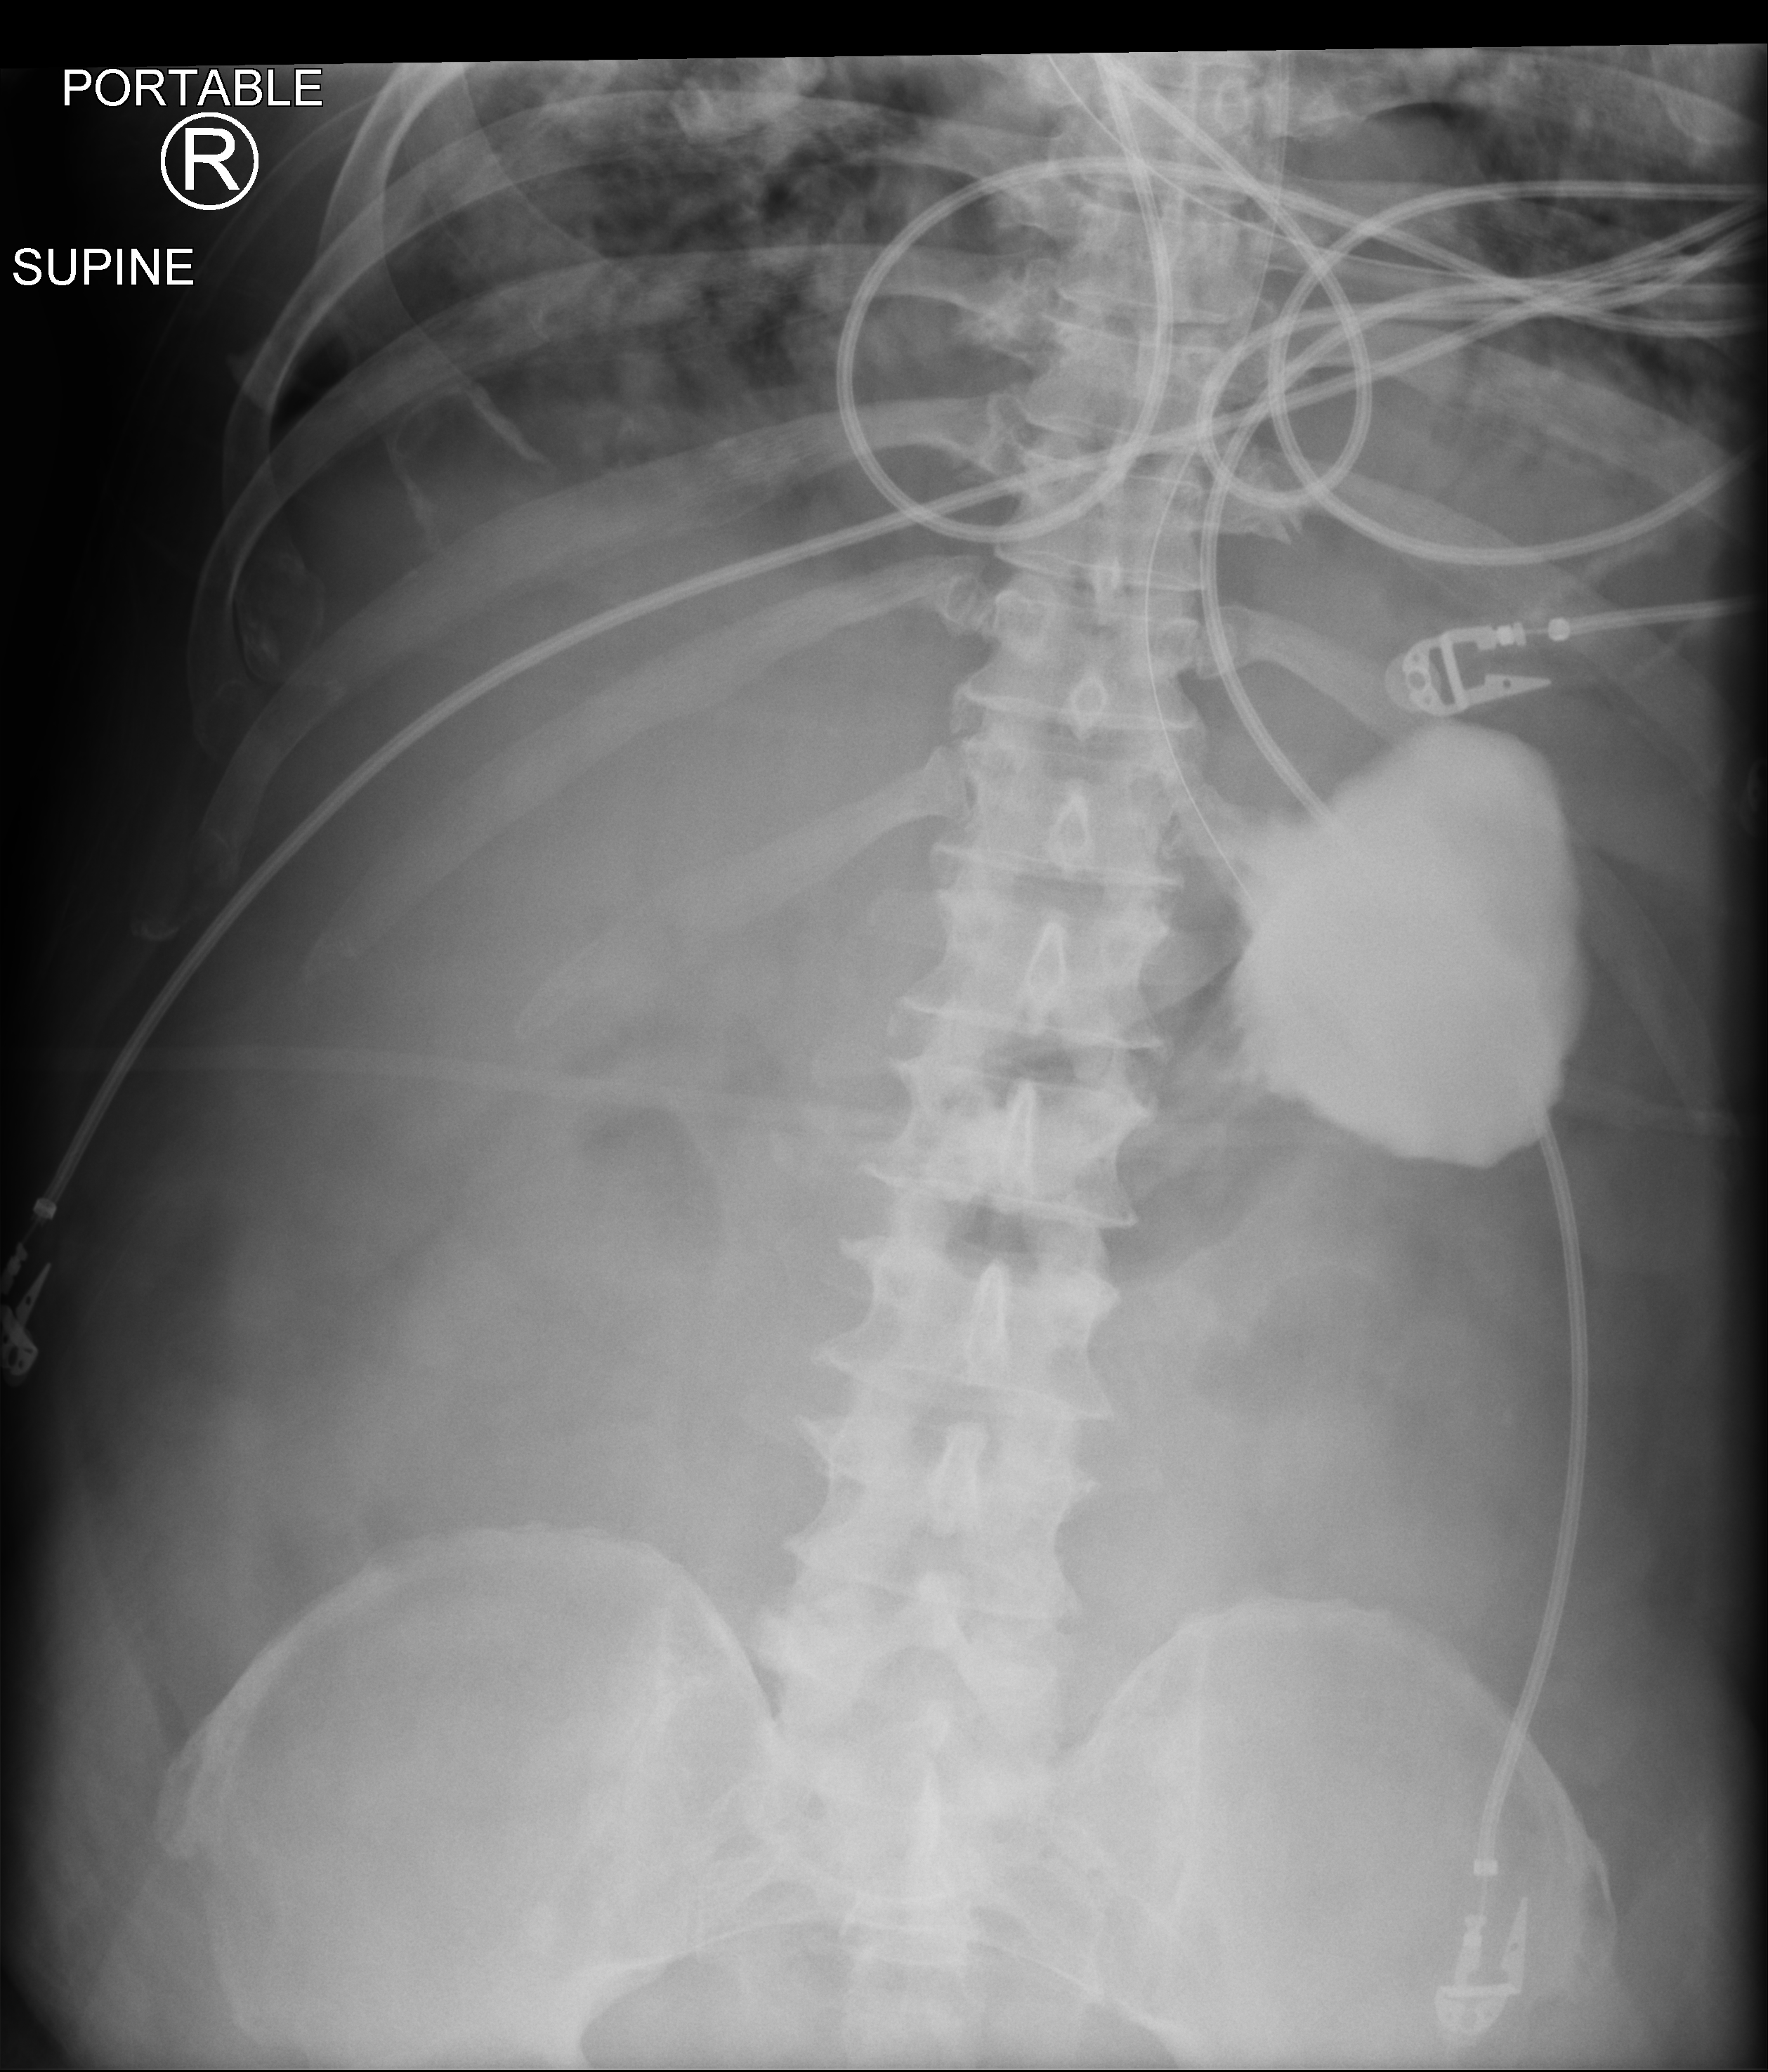
Bedside abdomen radiograph (computed radiography); anteroposterior (AP) projection. Male patient hospitalised with COVID-19, age 60–74 years.
Admission-level facts for this patient (not findings on this image; timing relative to this image not recorded): chronic kidney disease (admission record): no.